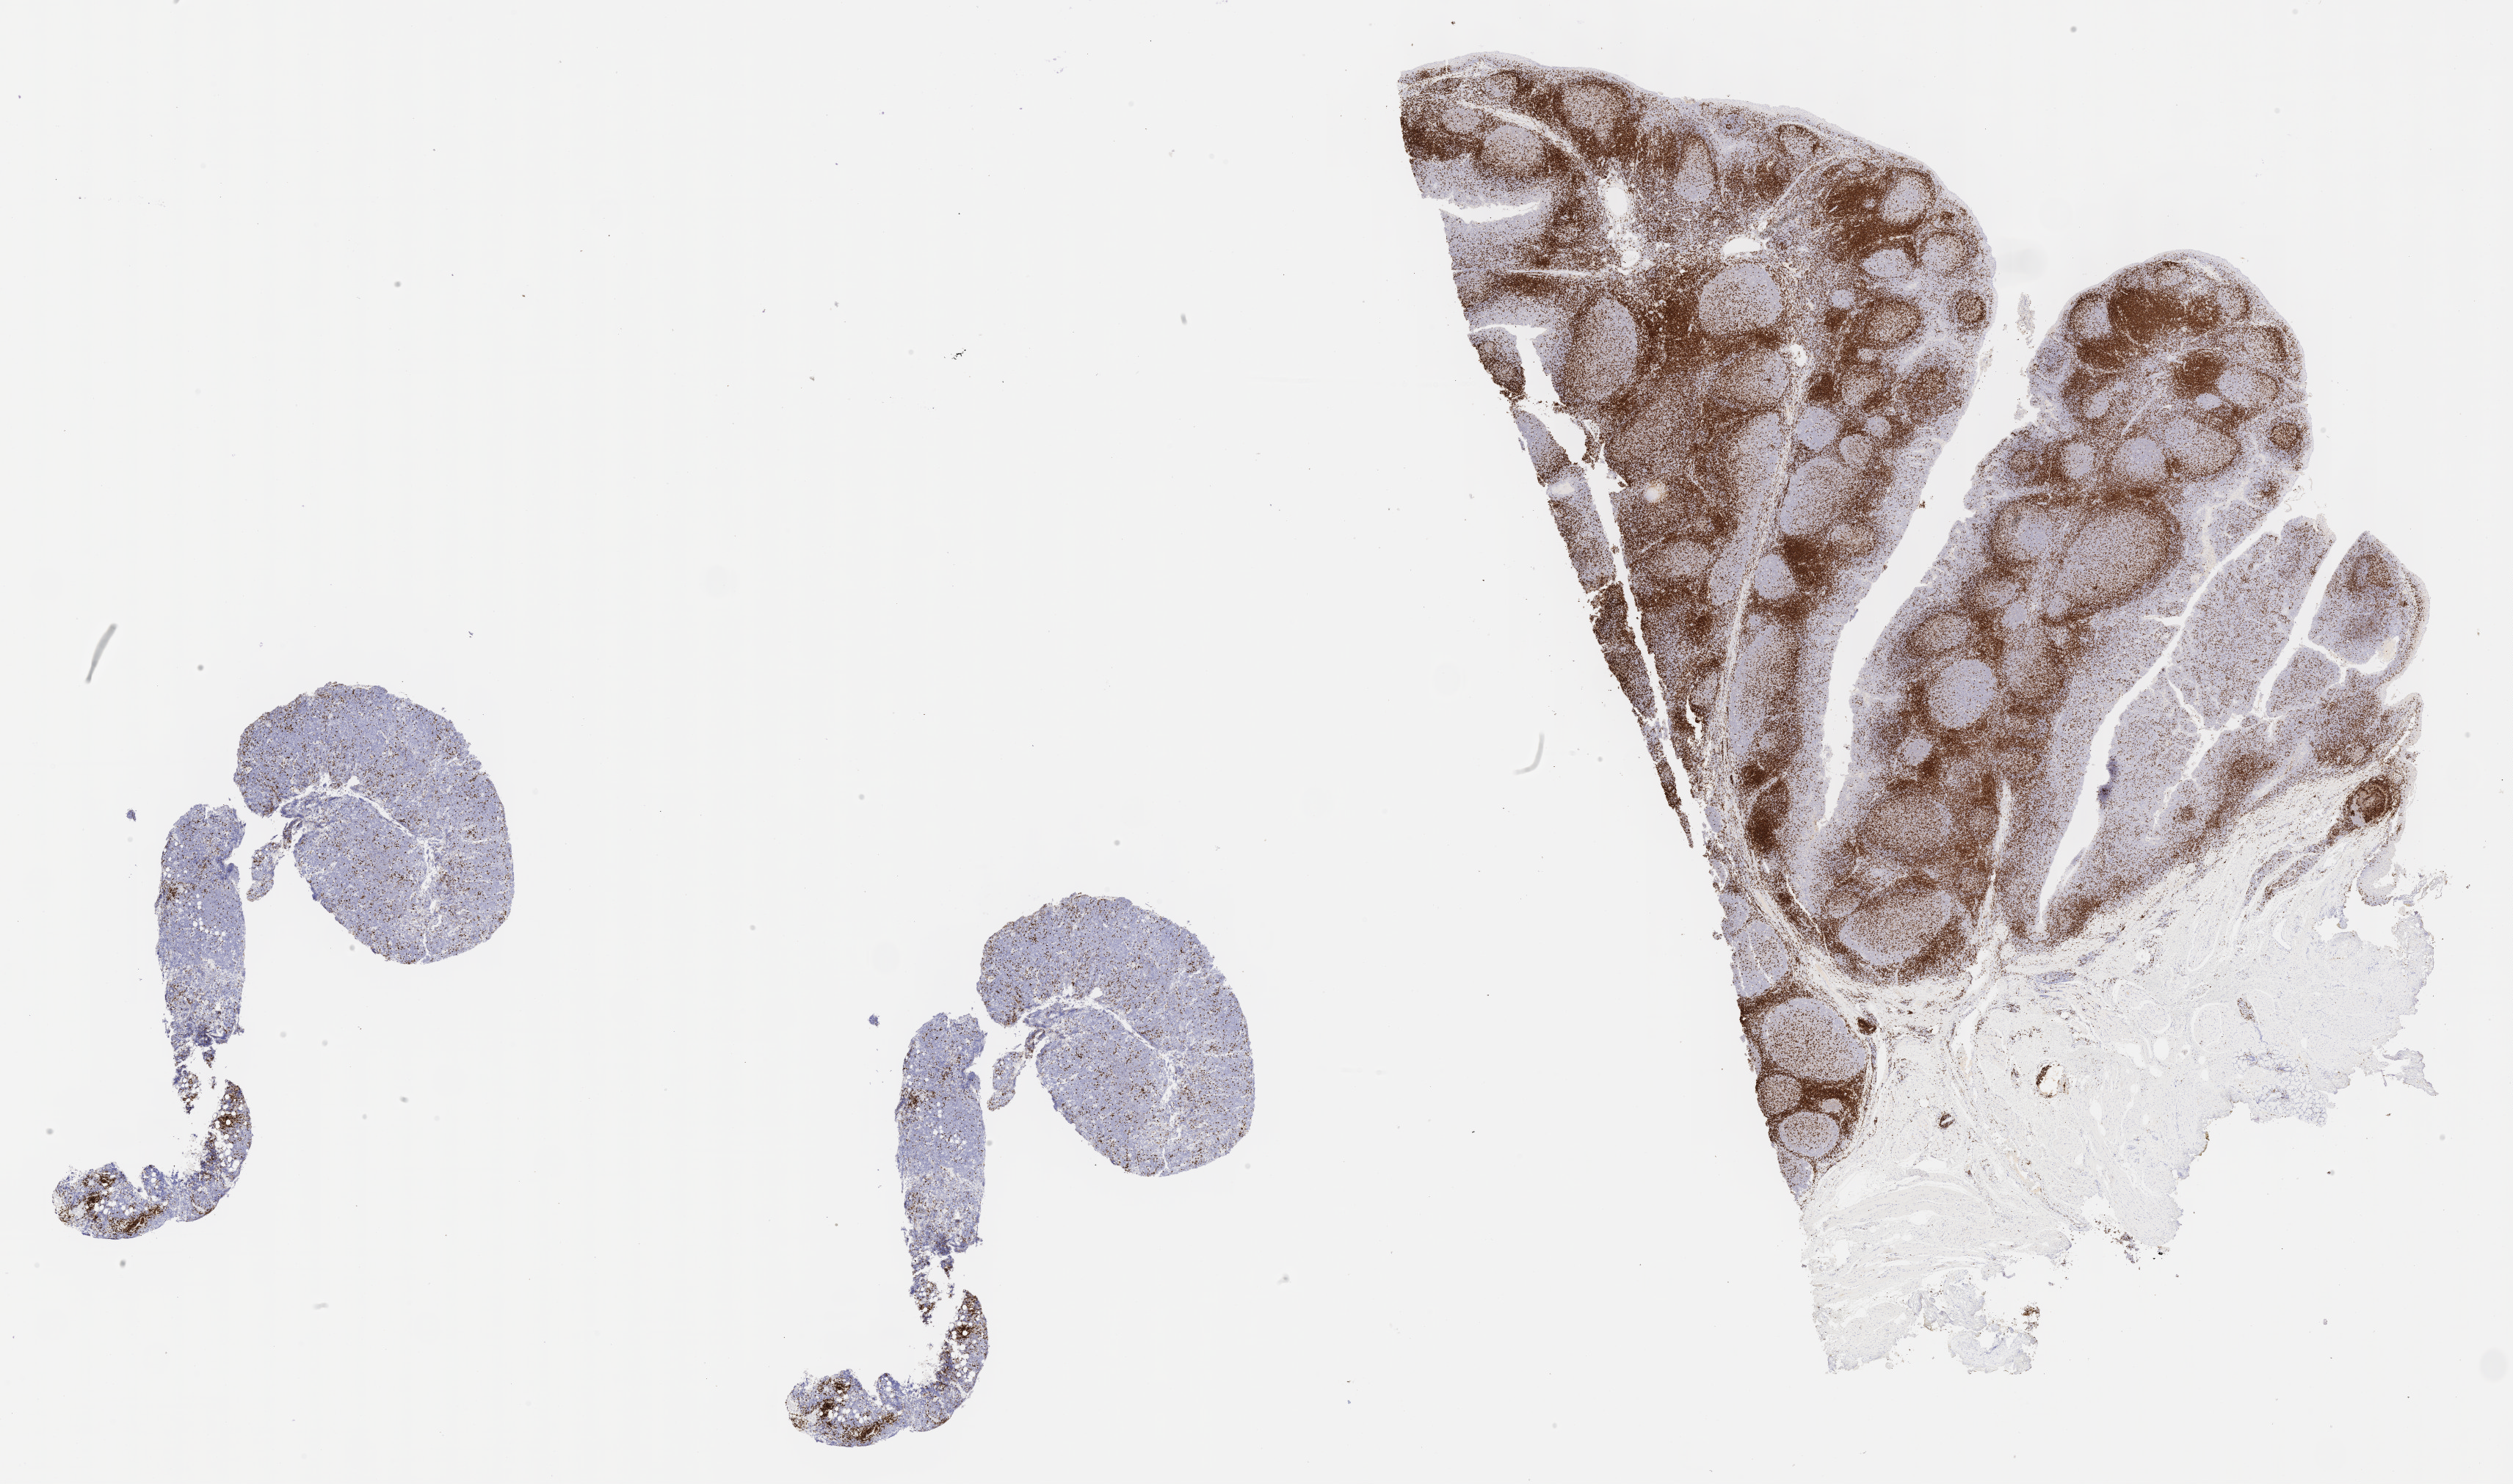
Immunohistochemistry (IHC) whole-slide image stained for CD3 — a low-resolution overview of the entire scanned area, about 27.7 x 16.3 mm. Tumor tissue. Anatomic site: head and neck. Patient female; 55 years old.
Histologic diagnosis: Burkitt lymphoma, NOS.